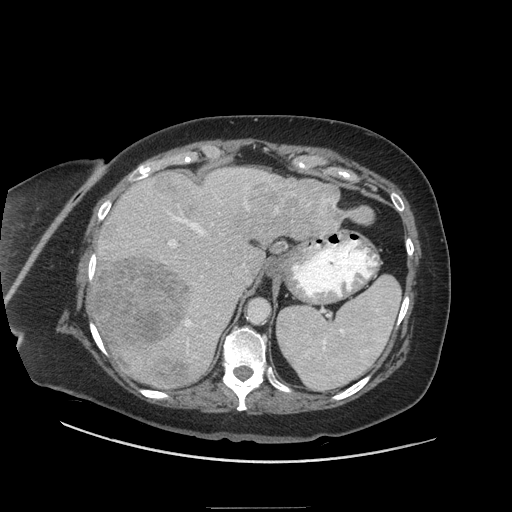
Contrast-enhanced abdominal CT (liver protocol), one axial slice; position 42 of 81 along the scan axis; reconstruction kernel STANDARD; 140 kVp; soft-tissue window (W 400 / L 40 HU); 512 × 512 image matrix, field of view 440 × 440 mm. Case-level facts recorded for this patient, not image findings: diagnosis: hepatocellular carcinoma (patient treated with transarterial chemoembolisation; whether this scan precedes or follows treatment is not stated here); TNM stage (as recorded): Stage-II; Child-Pugh class: A; tumour differentiation: moderately differentiated; tumour nodularity: multinodular.
Outlined on this slice (semi-automatically segmented with operator editing):
- liver parenchyma outside the tumour (the mass and vessels are separate outlines, so this box may not span the whole liver): bounding box [x1, y1, x2, y2] px = [88, 166, 338, 386]
- mass: [91, 172, 374, 389]
- liver vessels: [105, 170, 270, 358]